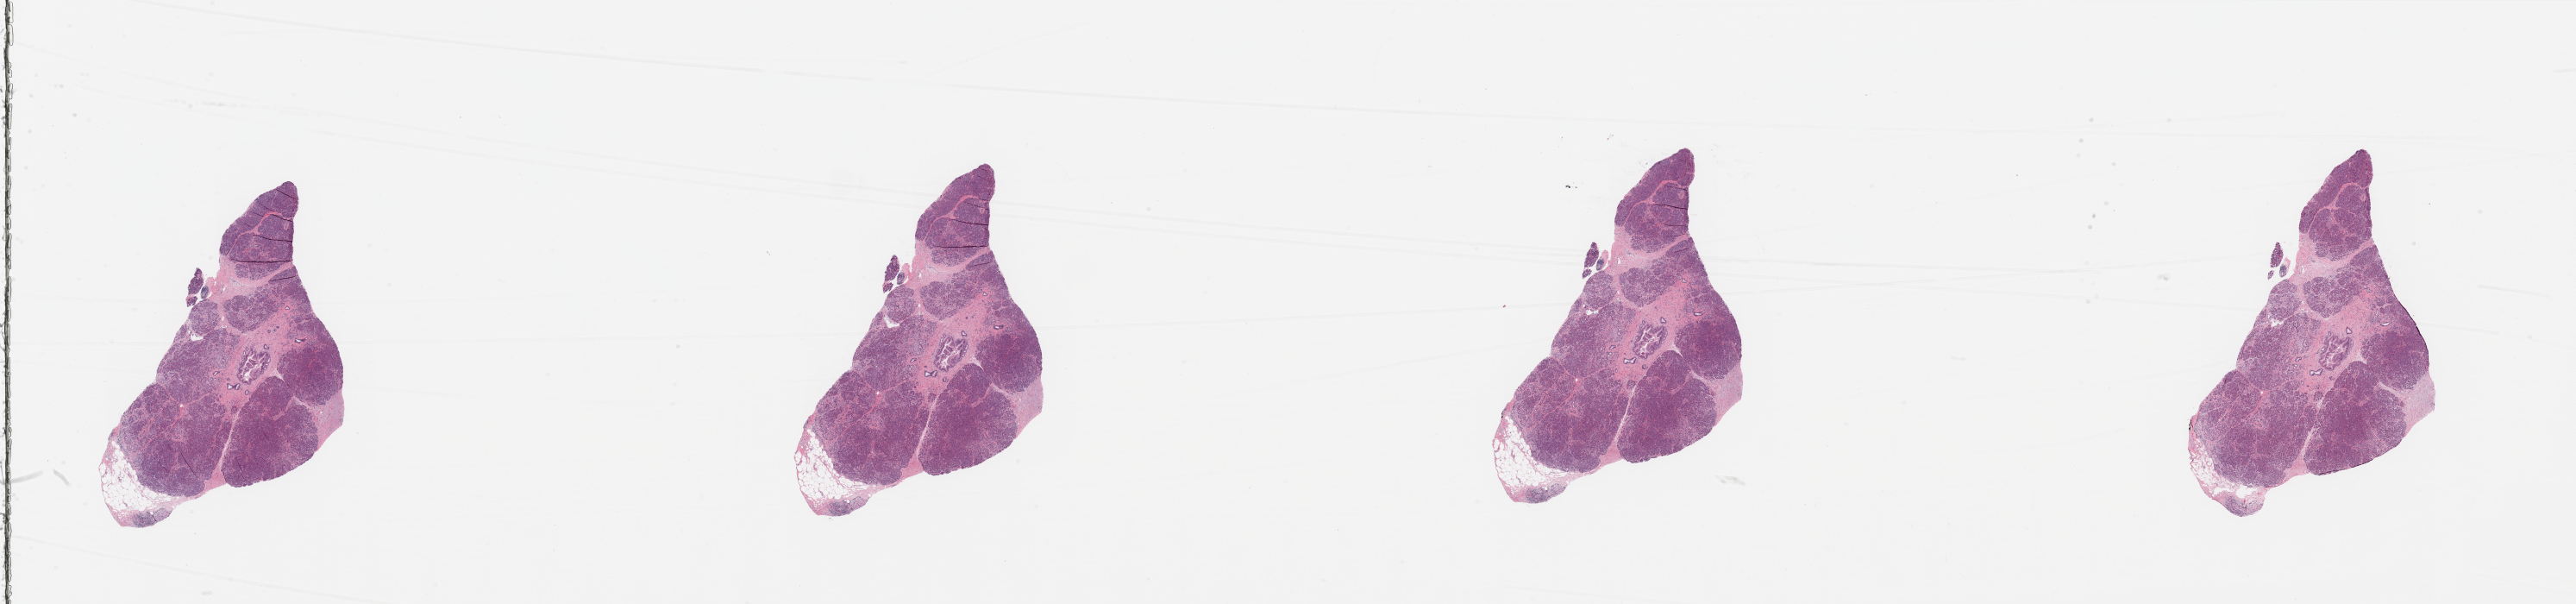
Whole-slide histology image, H&E — low-resolution overview of the scanned area, about 47.3 x 11.1 mm (slide scanned at 20x), pancreas, tumour tissue. Female, 69 y/o. Histologic grade: G2 (moderately differentiated).
AJCC pathologic stage: IIB. Diagnosis: Infiltrating duct carcinoma, NOS. Primary tumour site (as recorded): head.